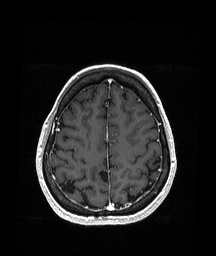
Brain MRI from a brain-tumour surgery series, one axial slice; T1-weighted post-contrast; 216 × 256 image matrix, field of view 211 × 250 mm. From the clinical record (not read from this slice): histopathology: Oligodendroglioma; WHO grade: 2; IDH mutation: yes; tumour location: Right Parietal.
Structures marked on this image (manually delineated by an expert):
- previous resection cavity: box from (x=94, y=157) to (x=109, y=180) px